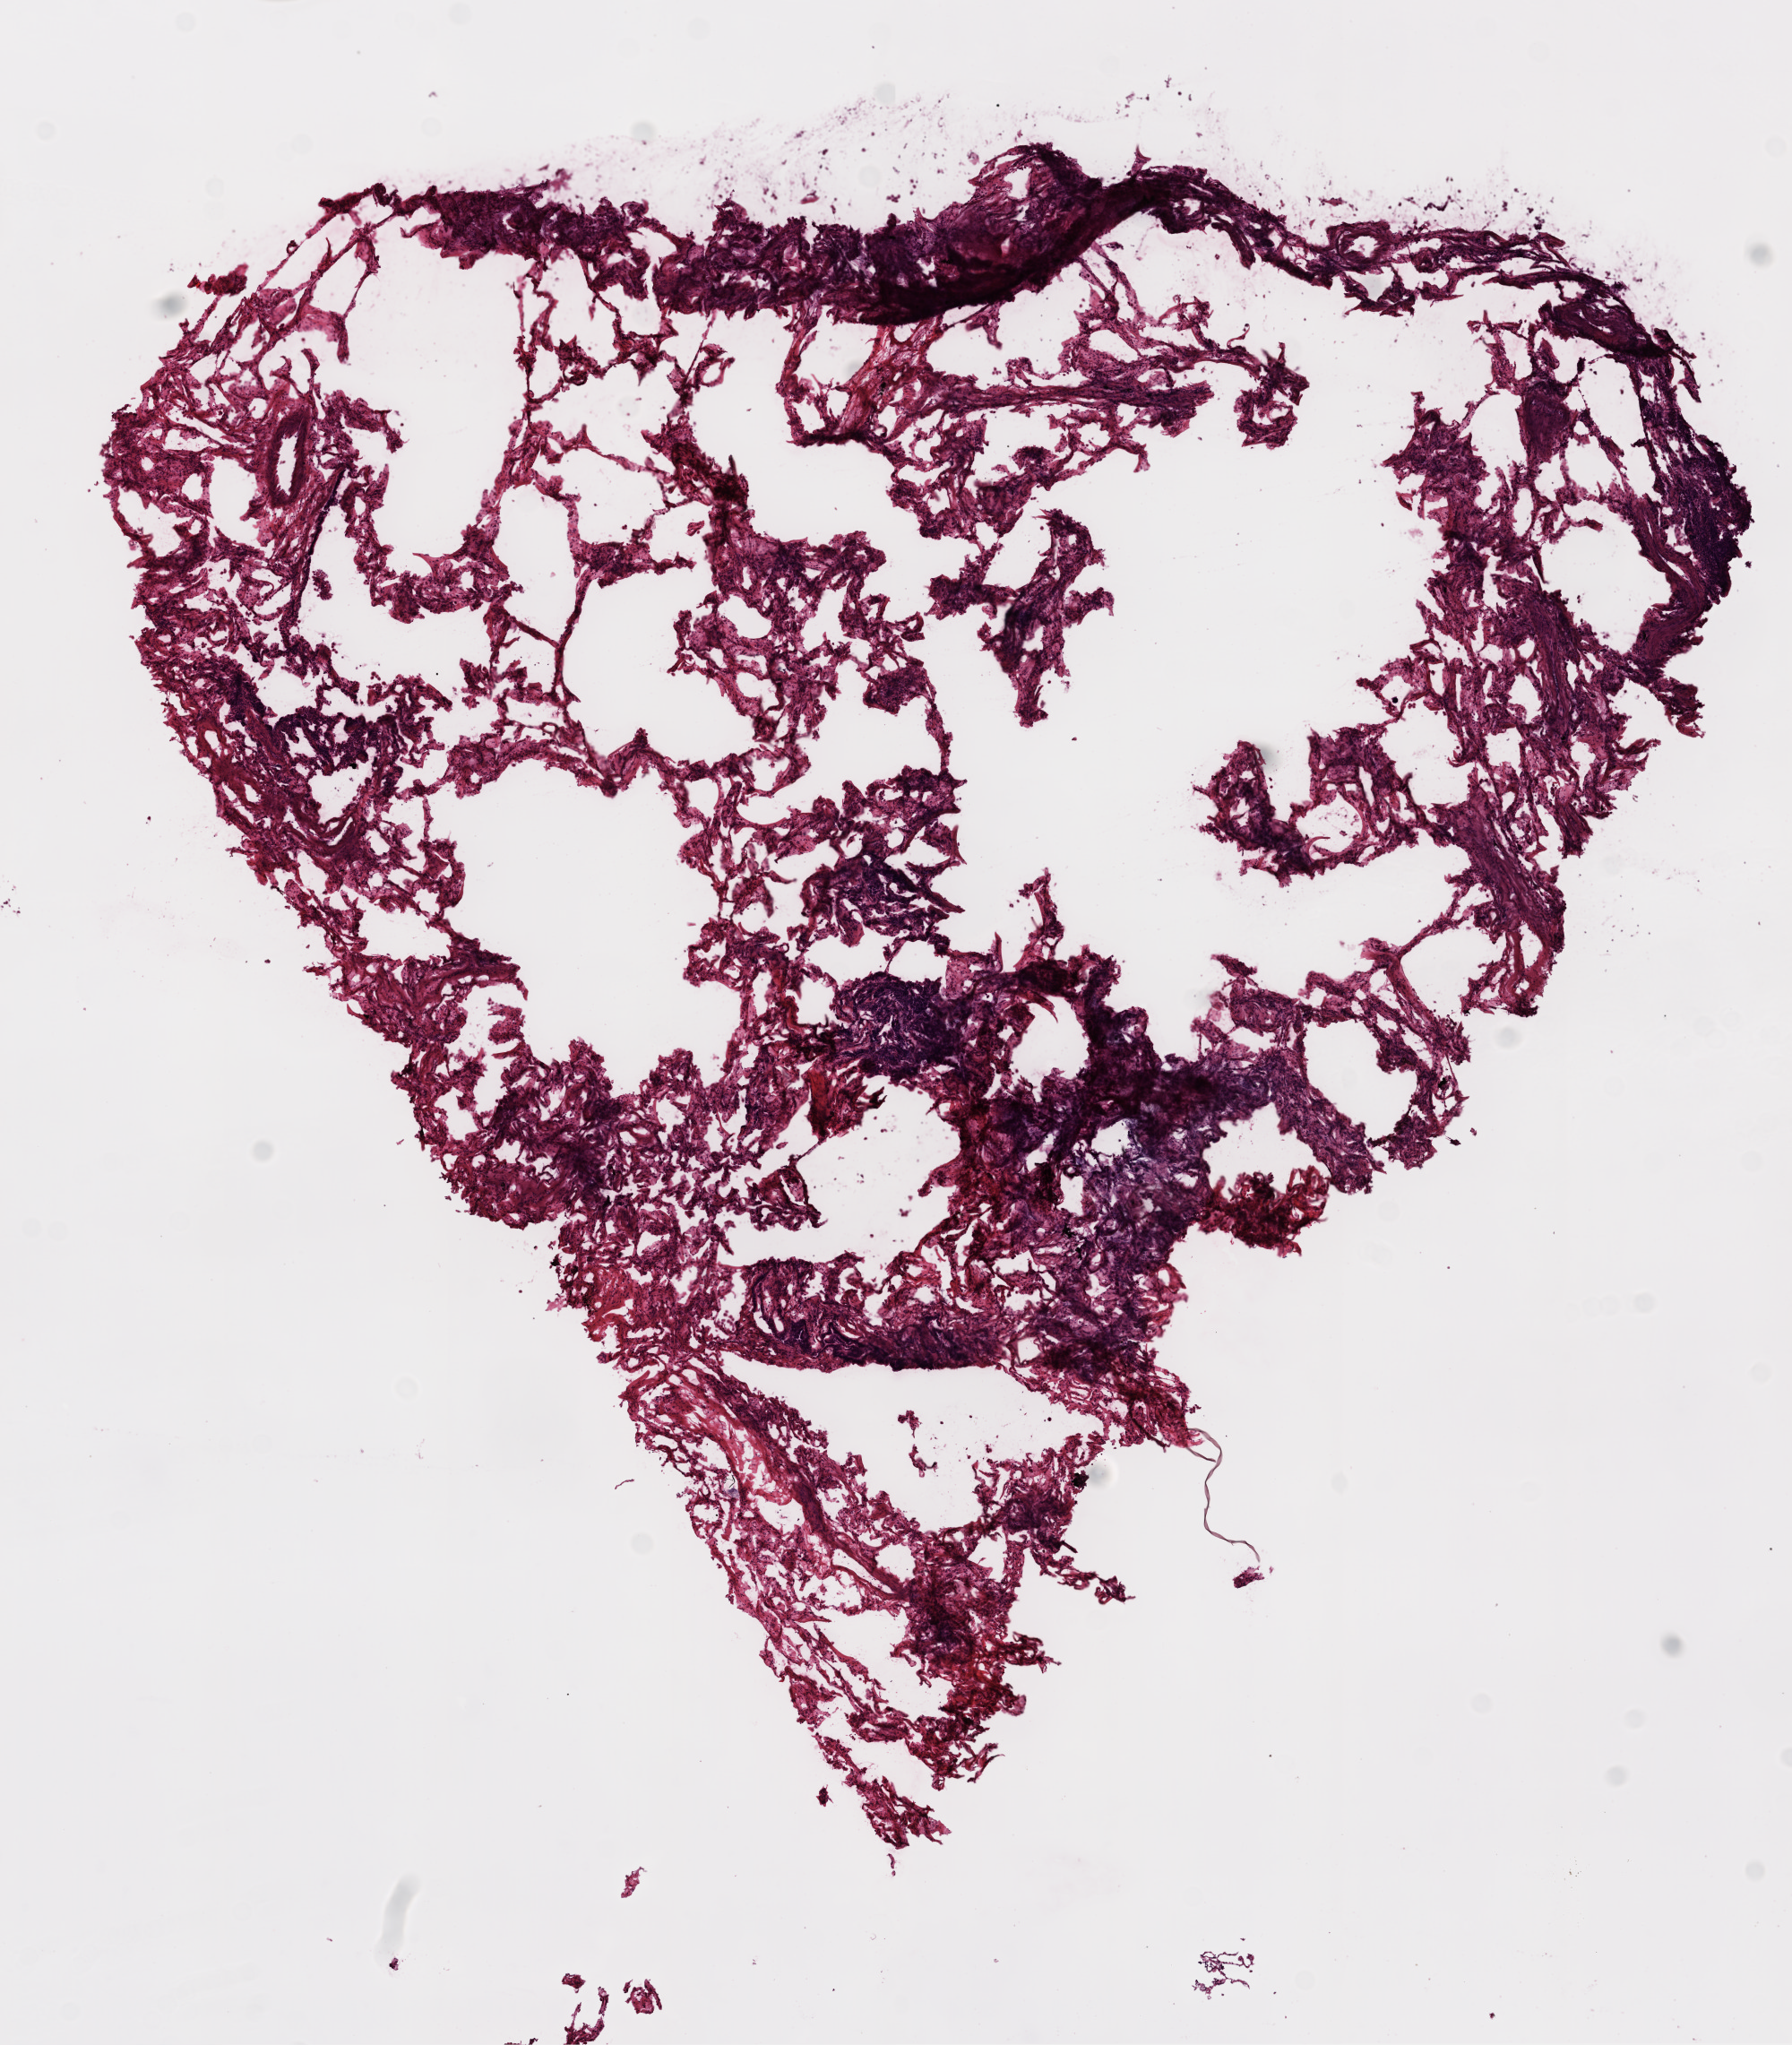
Digitized Hematoxylin and eosin (H&E) stained tissue section (whole slide) — low-resolution overview of the scanned area, about 8.0 x 9.2 mm, frozen section from the top of the tissue portion, solid tissue normal (non-tumour tissue) sample from the lung. Male patient; age at initial diagnosis 84 years.
This section: solid tissue normal (non-tumour) sample from the same patient. Patient diagnosis: Squamous cell carcinoma, NOS.